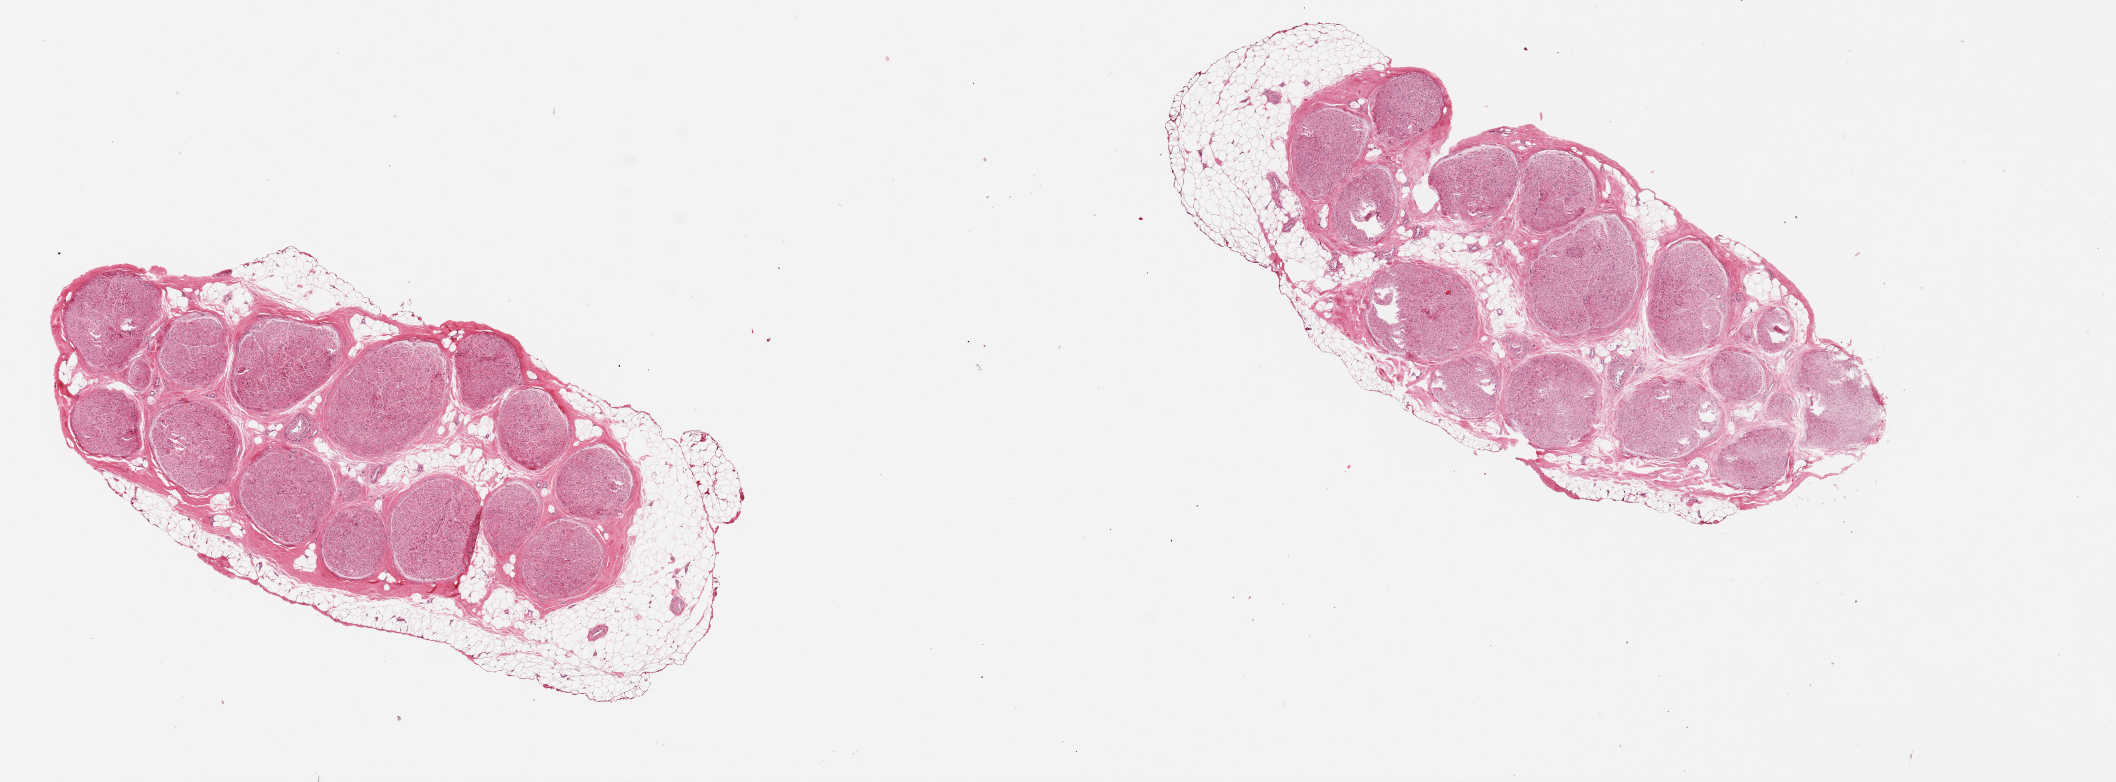
Digitized hematoxylin and eosin (H&E)-stained section — low-resolution overview of the scanned area, about 16.7 x 6.2 mm; PAXgene-fixed, paraffin-embedded tissue; sampled site (target tissue): tibial nerve; donor tissue sample. Donor sex: female.
* pathologist's review note for this sample: 2 pieces, encased in fat up to 1 mm thick